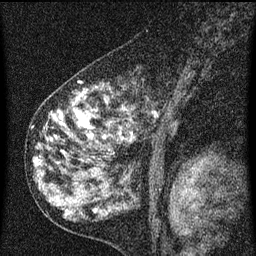
Breast MRI (dynamic contrast-enhanced), one sagittal slice; position 36 of 60 along the scan axis; dynamic contrast-enhanced series, image 2 of 3 at this slice position (ordered by acquisition); 1.5 T; TE 4.2 ms, TR 8 ms; 256 × 256 image matrix, field of view 180 × 180 mm. Patient: female, 55 years.
Structures marked on this image (semi-automatically segmented with operator editing):
- analysis volume of interest (the breast-tissue region the enhancement analysis was run in; not a lesion): bounding box <42,72,183,155> (left, top, right, bottom; pixels)
- tumour enhancement mask (voxels above the 70 % enhancement threshold inside the analysis volume of interest): <54,98,123,141>